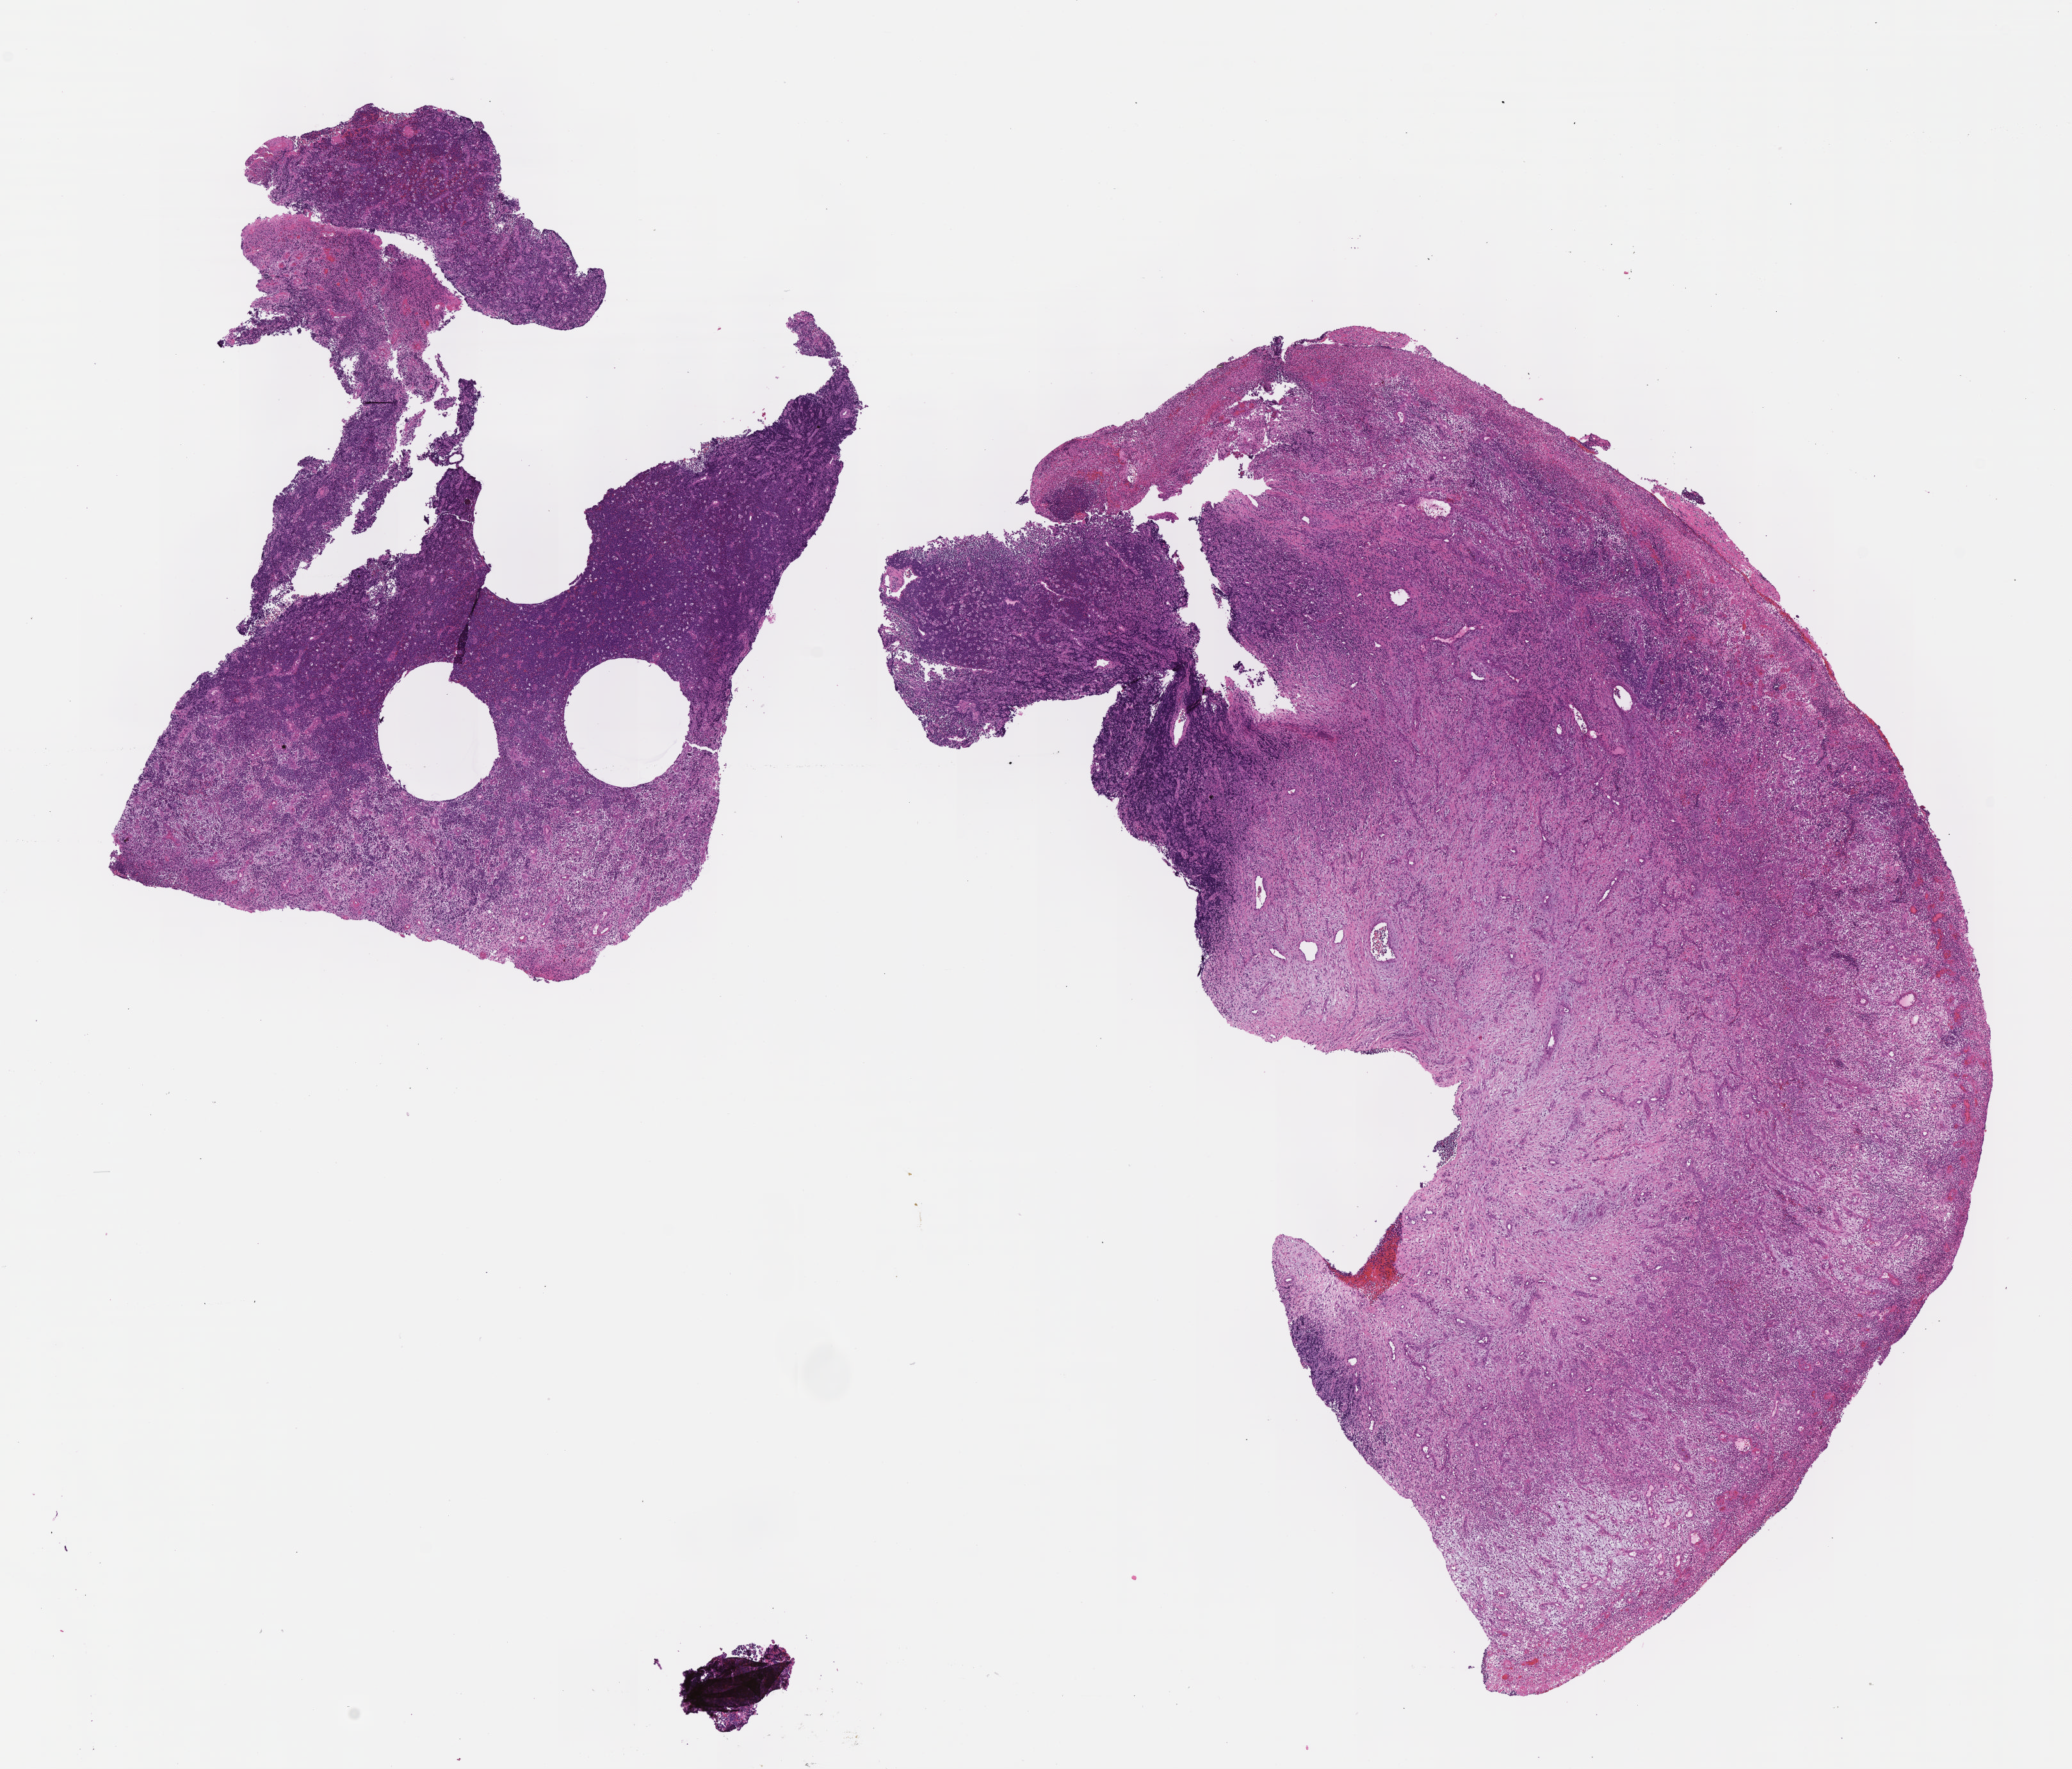
Digitized H&E-stained section, low-resolution overview of the scanned area, about 13.1 x 11.2 mm; formalin-fixed, paraffin-embedded (FFPE) tissue; specimen: primary tumor; site: cranium. Female patient, aged 11. Composition of this section per pathologist review: tumor cells 30%, tumor nuclei 60%, stromal cells 10%, necrosis 20%, normal cells 40%. Infiltration values recorded for this section: lymphocyte infiltration 50%, monocyte infiltration 20%, neutrophil infiltration 20%.
Ann Arbor stage (patient): Stage I. Diagnosis: Burkitt lymphoma, NOS. Section: top of the tissue portion.